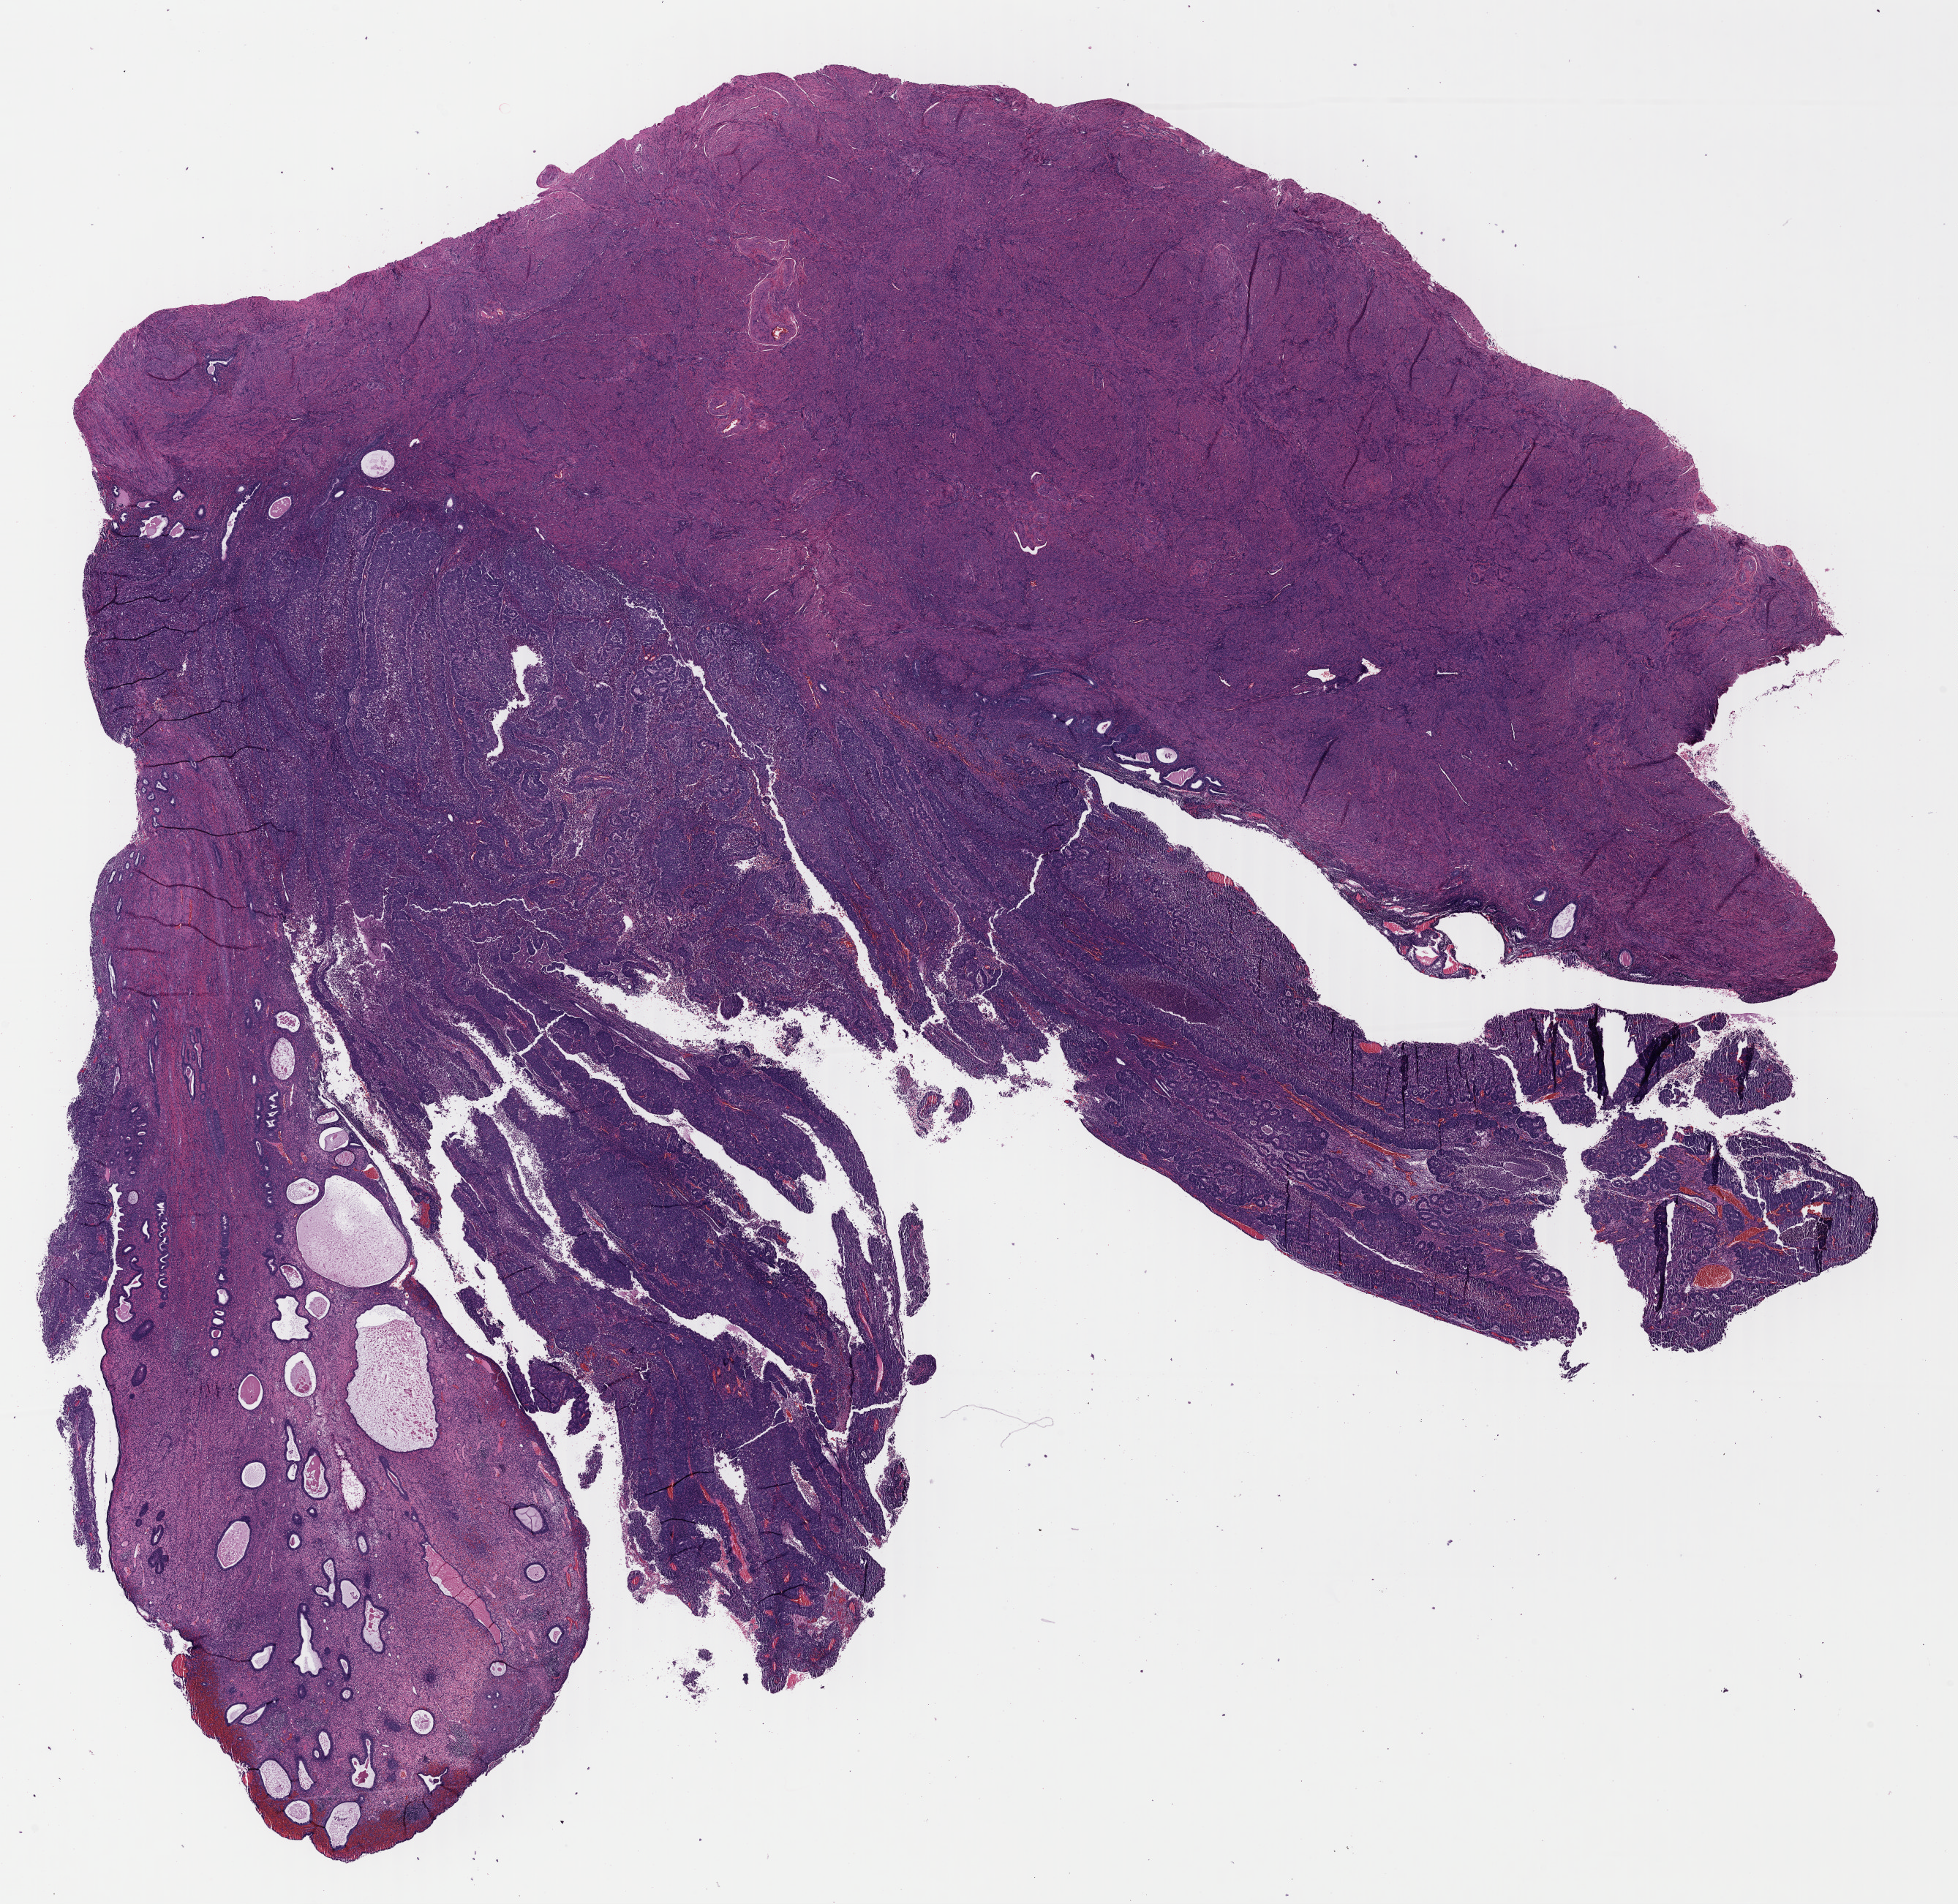
Hematoxylin and eosin (H&E) stained whole-slide image — a low-resolution overview of the entire scanned area, about 21.0 x 20.5 mm (acquisition: 40x scan), formalin-fixed paraffin-embedded (FFPE) diagnostic section, uterus, primary tumour sample. Patient: female, age at initial diagnosis 61 years.
Pathologic diagnosis: Endometrioid adenocarcinoma, NOS (endometrium).